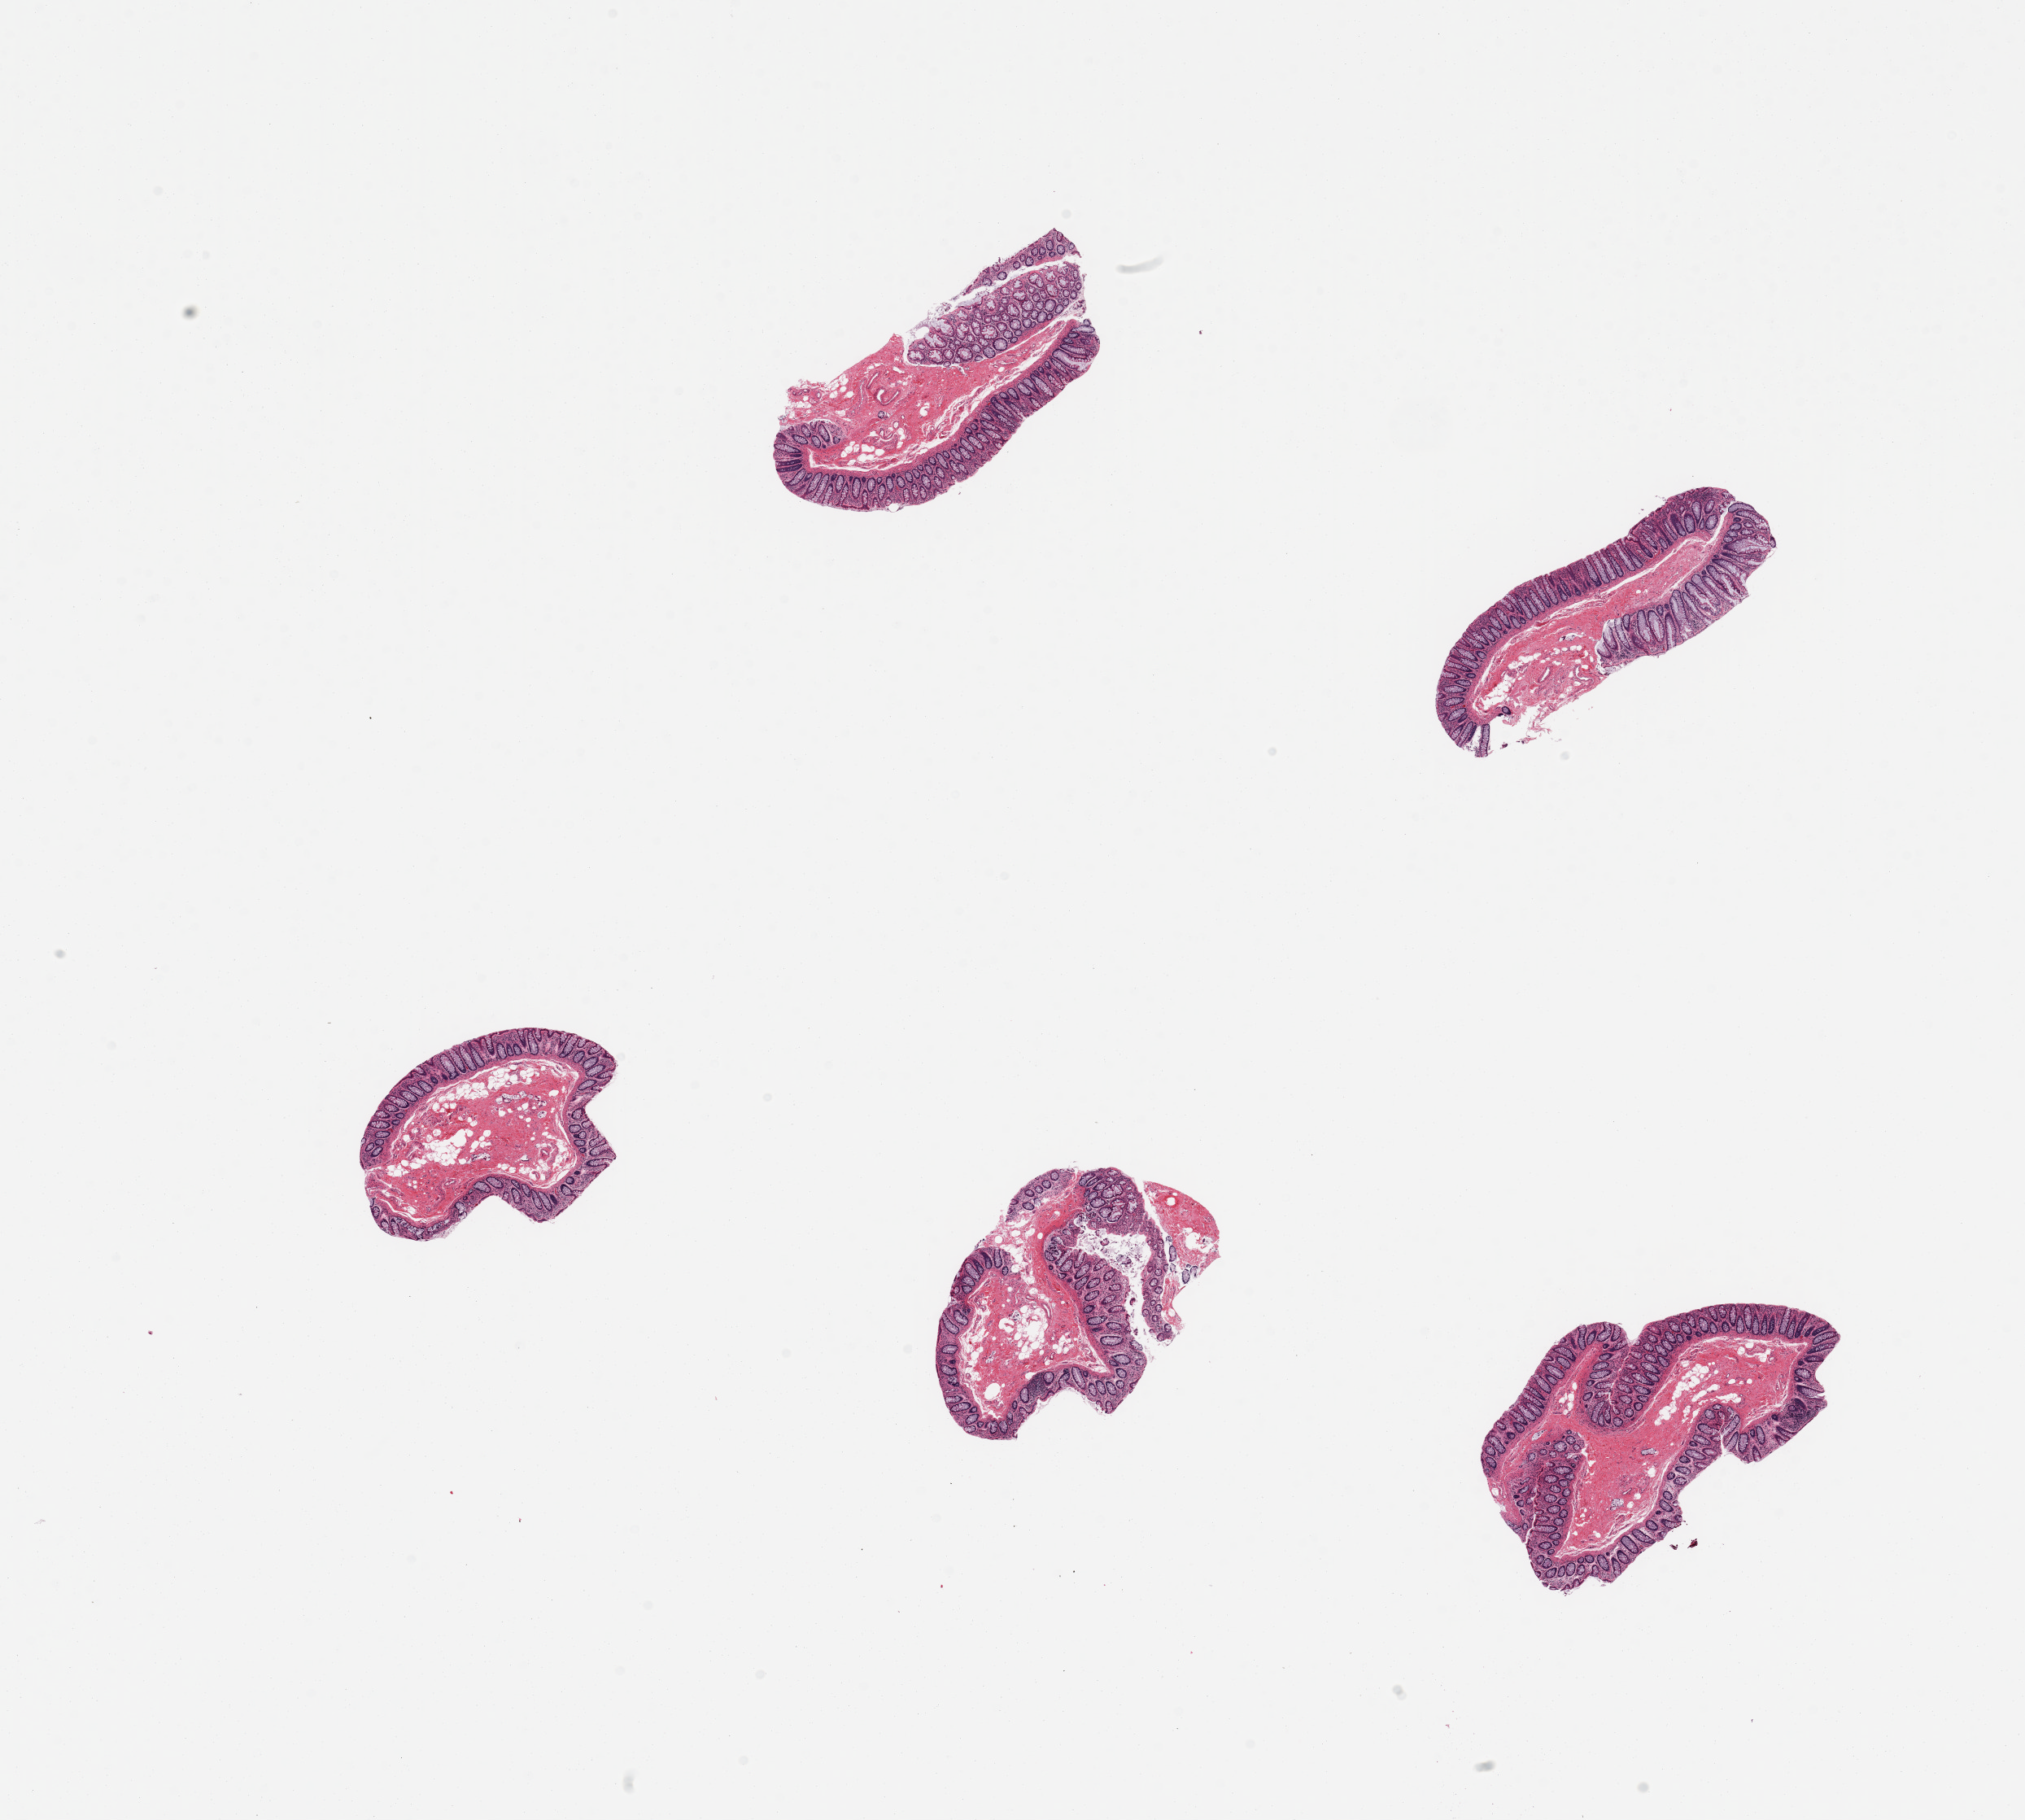
Whole-slide image, hematoxylin and eosin (H&E) stain, low-resolution overview of the scanned area, about 19.7 x 17.7 mm (from a 20x scan); PAXgene-fixed paraffin-embedded (PFPE) section; section of sigmoid colon (target tissue); donor tissue sample. Male donor.
Review note (as recorded): 5 pieces; mucosa only; (this could be transverse colon).